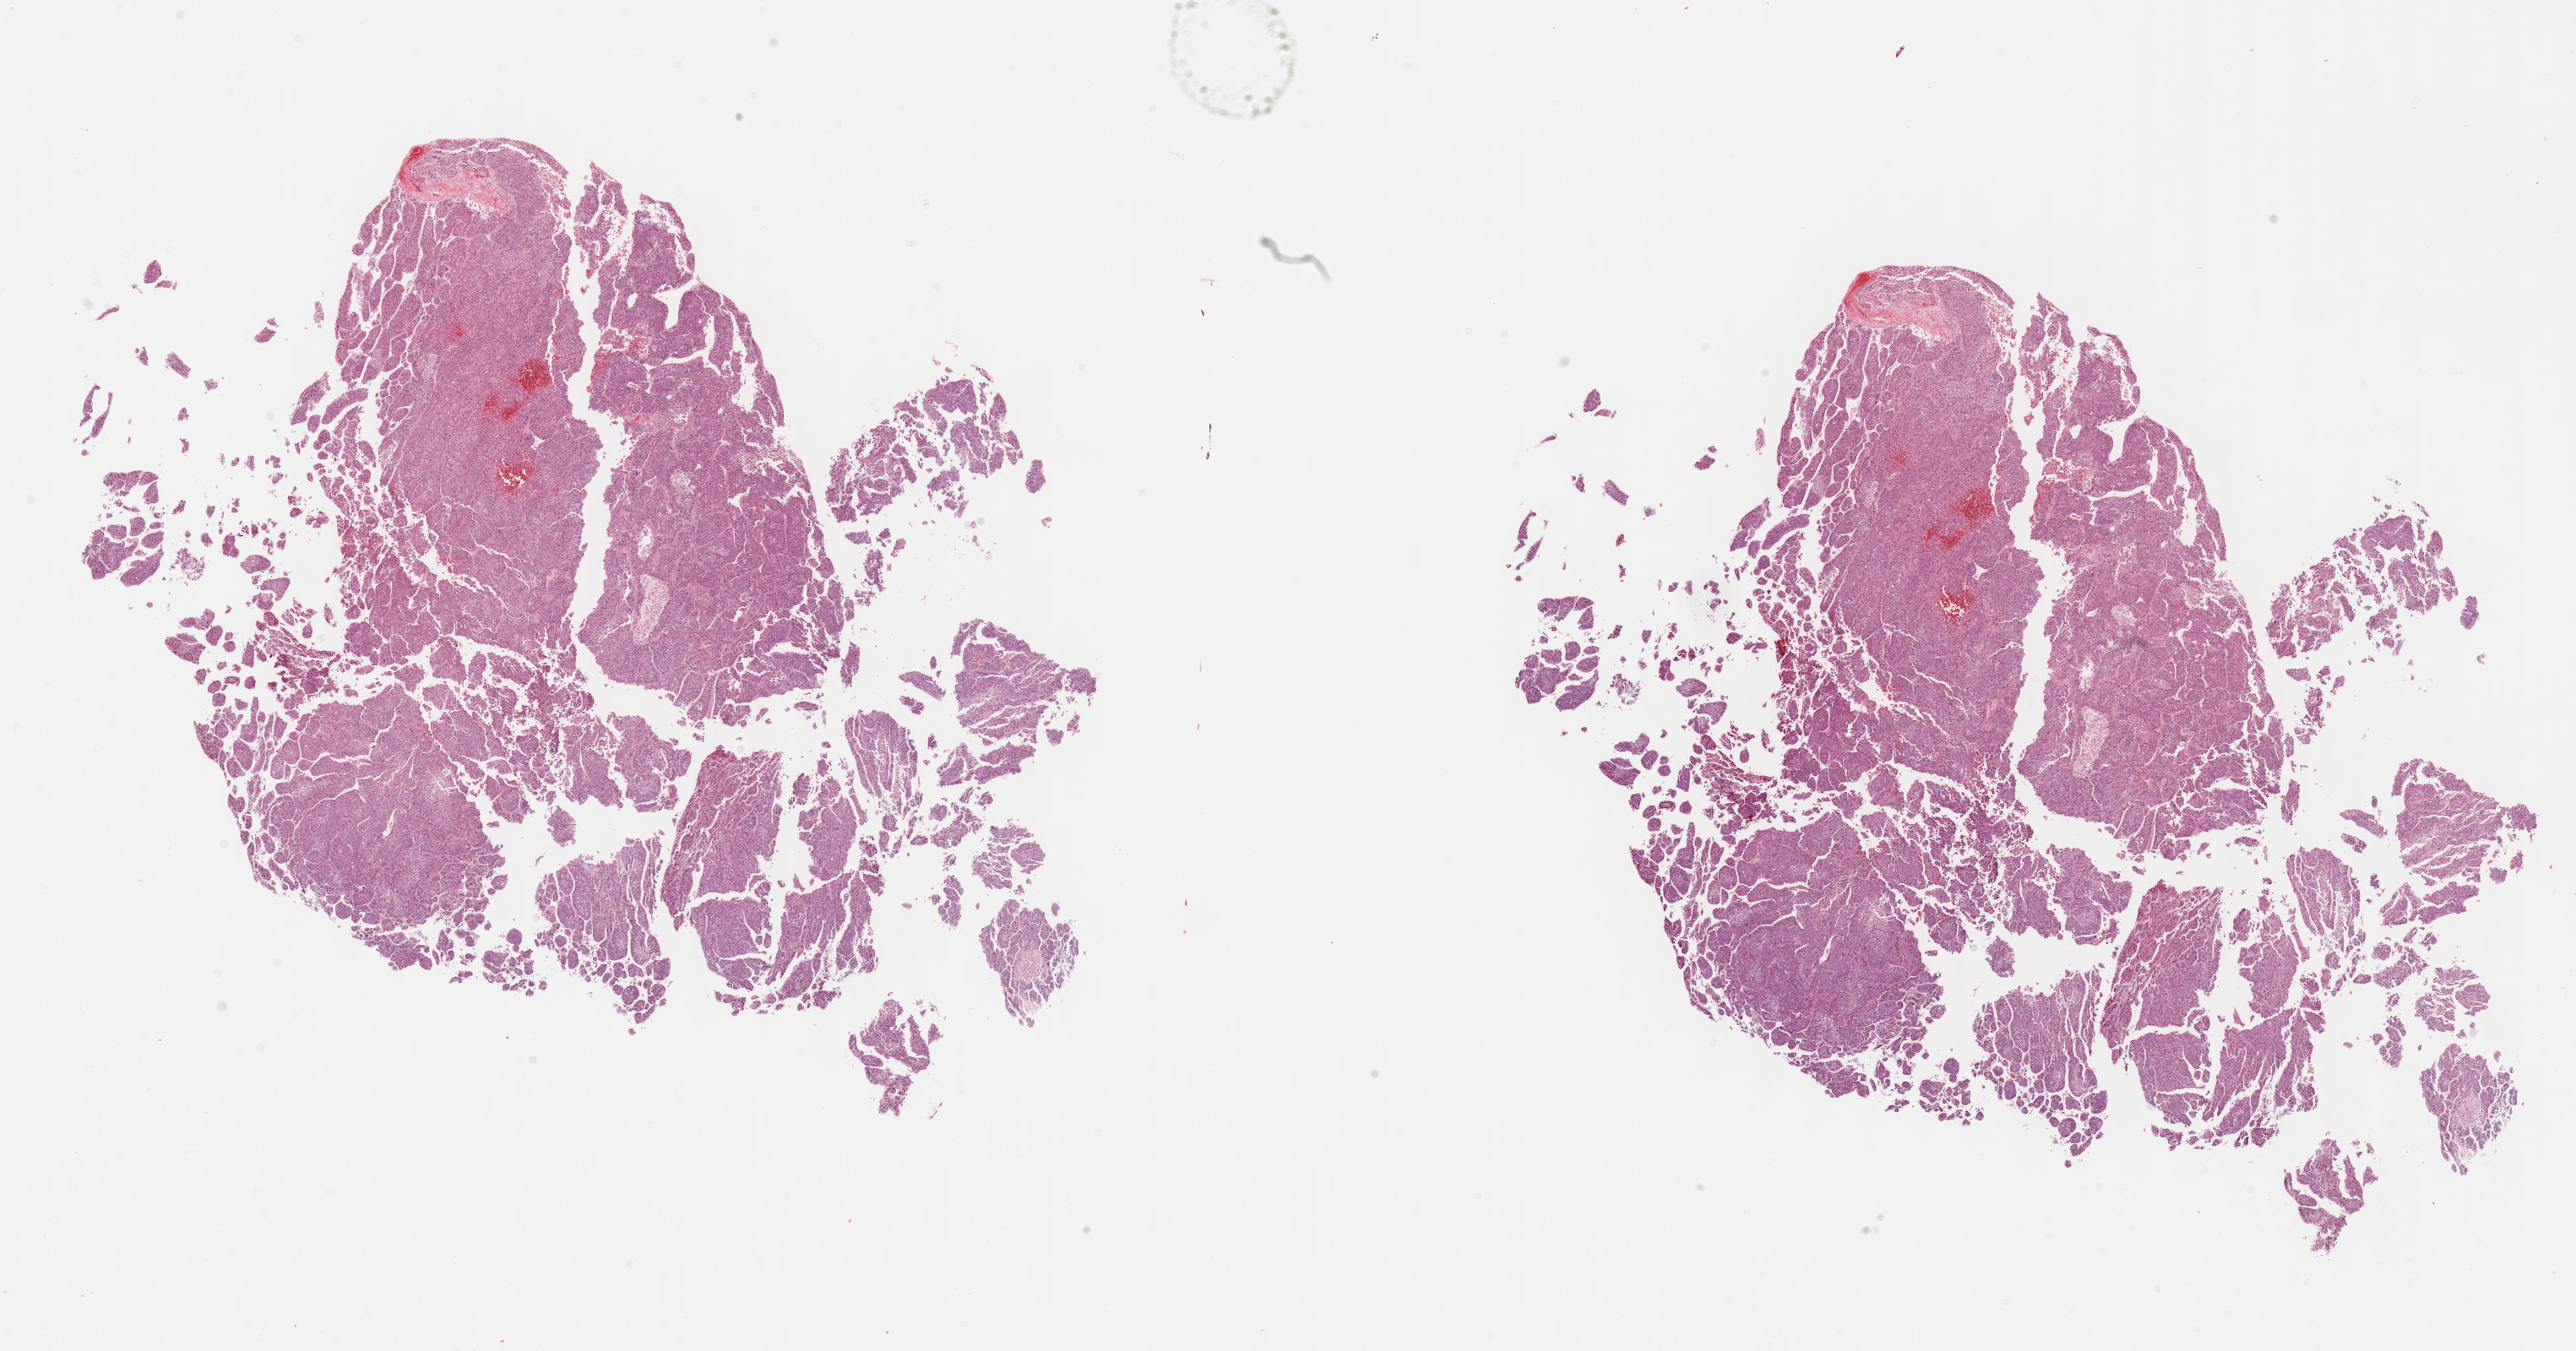
Whole-slide histology image, H&E-stained, a low-resolution overview of the entire scanned area, about 24.6 x 12.9 mm (acquisition: 40x scan); formalin-fixed paraffin-embedded (FFPE) diagnostic section; primary tumour sample from the liver. Female patient; age at initial diagnosis 63 years. Histologic grade: G4 (undifferentiated).
- AJCC pathologic stage: I
- pathologic diagnosis: Hepatocellular carcinoma, NOS